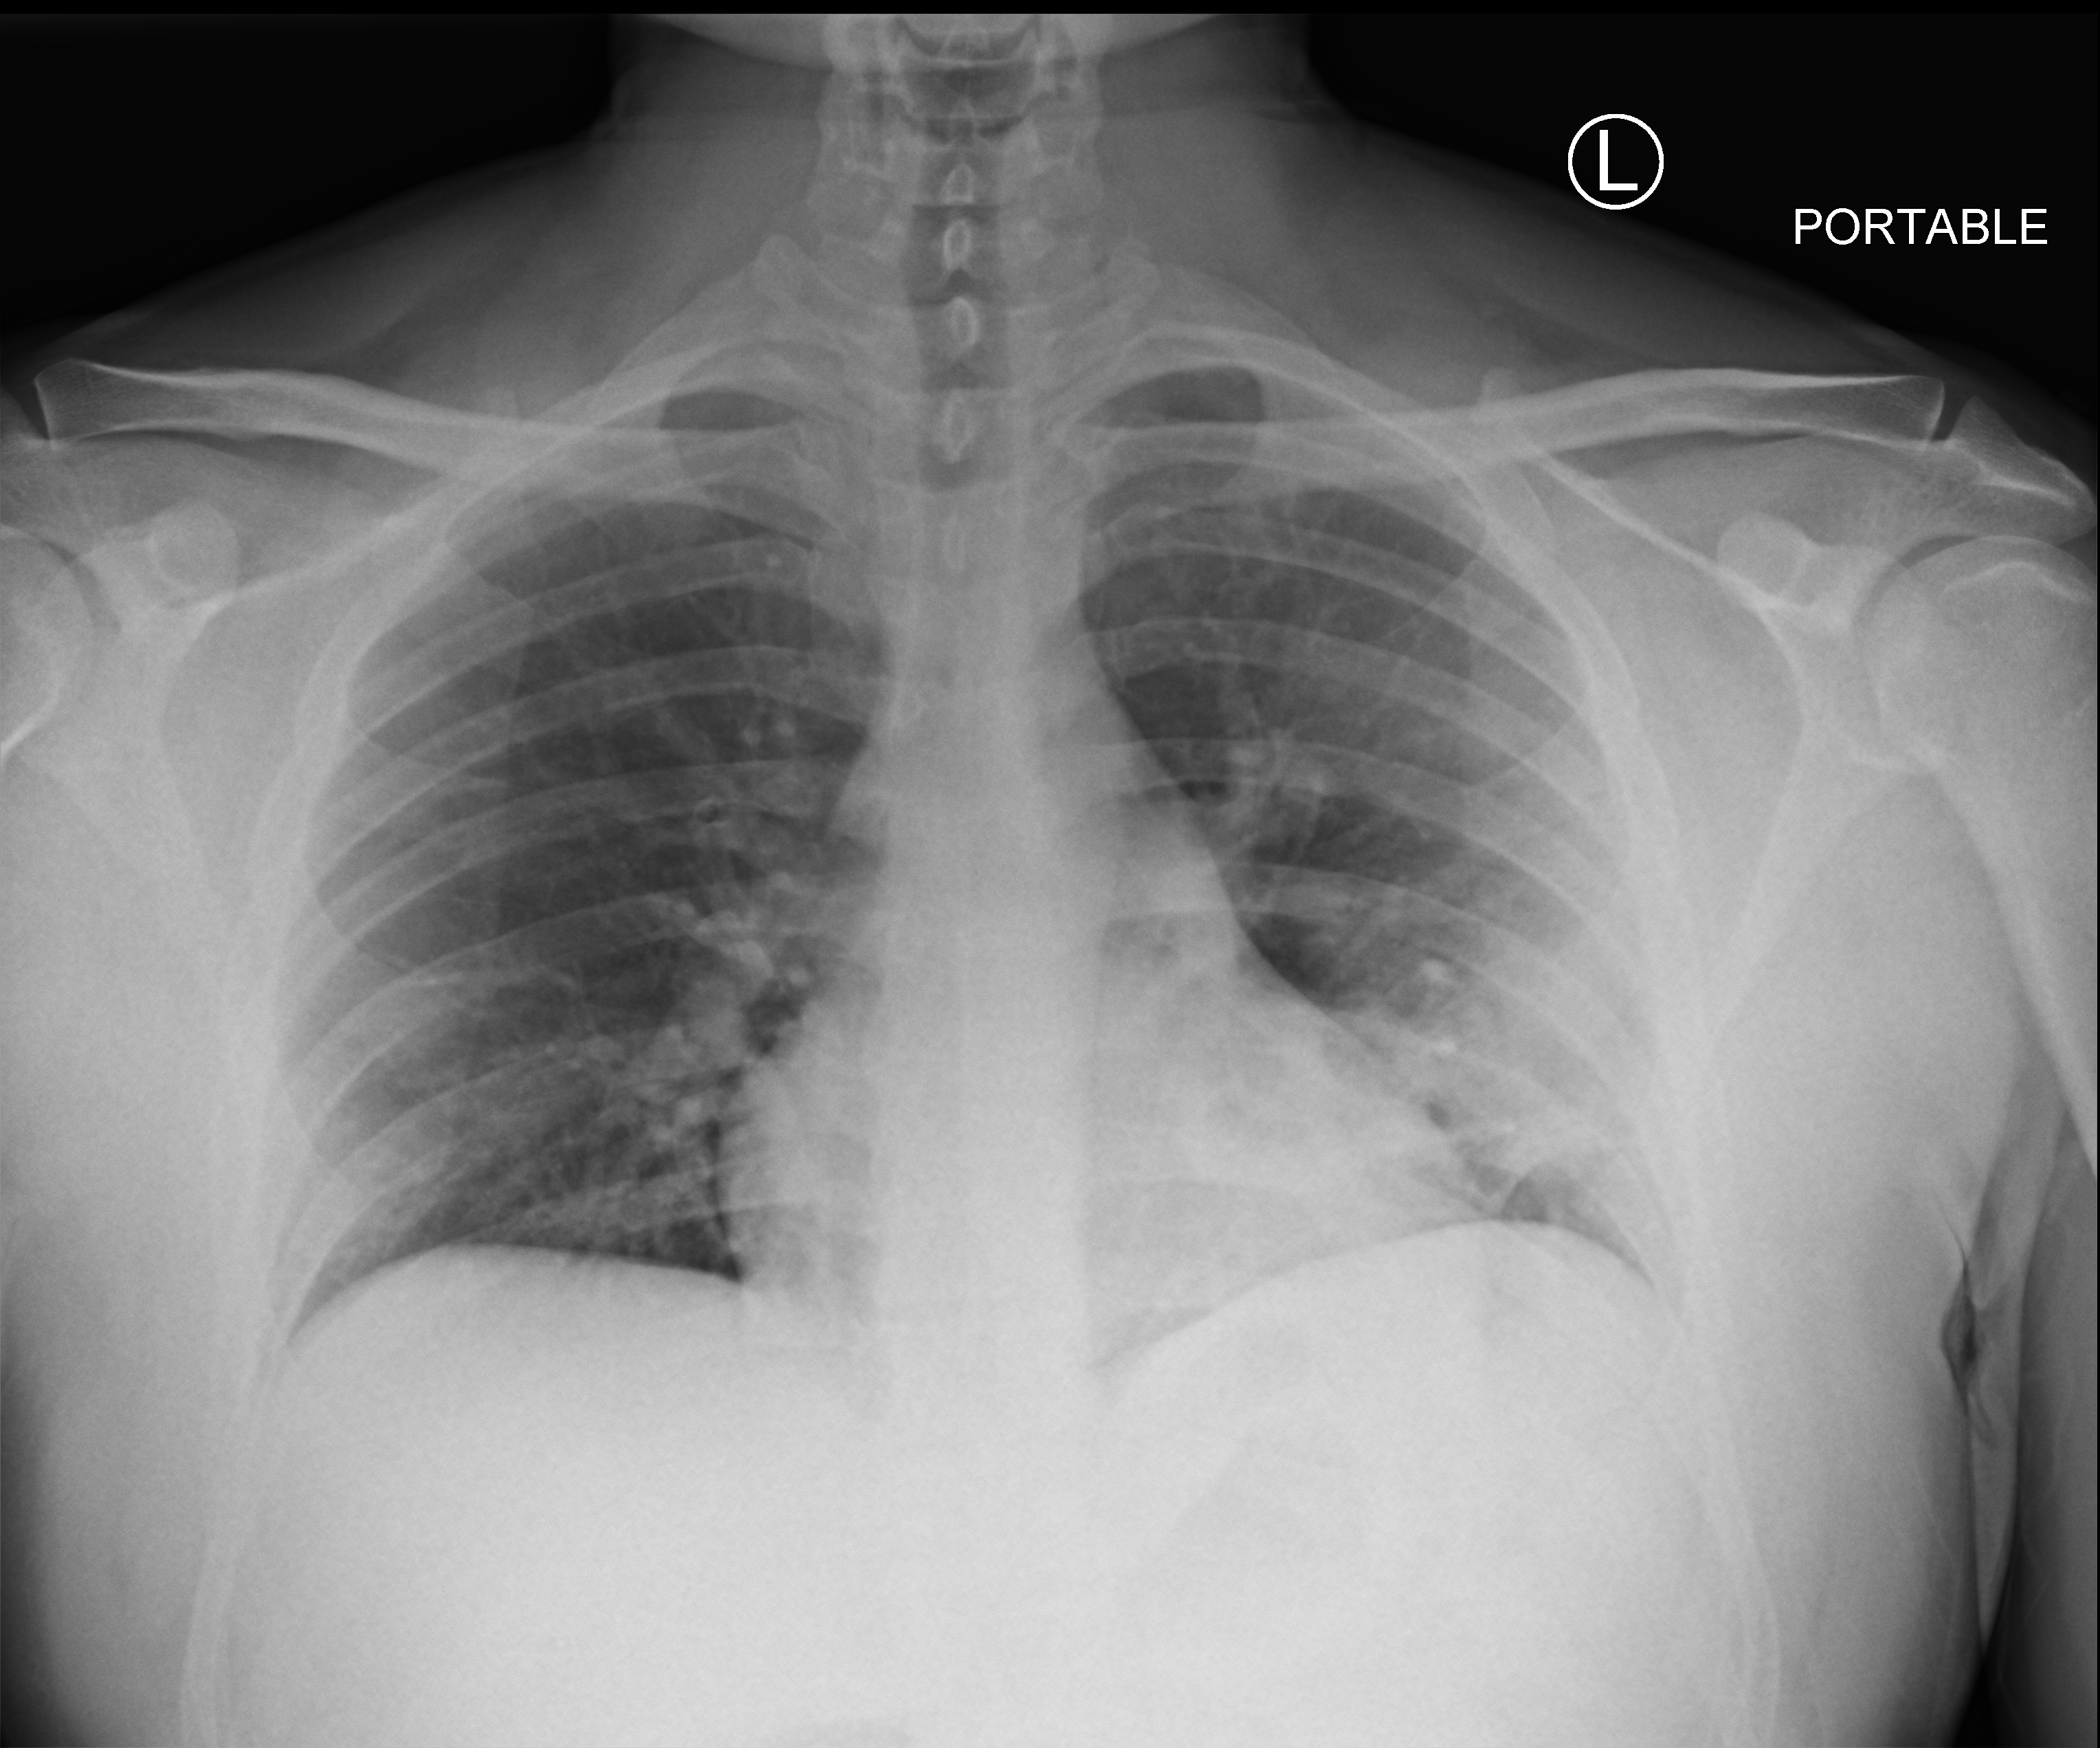
Chest X-ray (portable), anteroposterior (AP) projection. Patient hospitalised with COVID-19; male, aged 18–59 years.
Hospital-stay facts (about this admission, not read from this image; timing relative to this image not recorded):
- smoking status (admission record): never
- mechanically ventilated during this hospital stay: no
- COPD (admission record): no